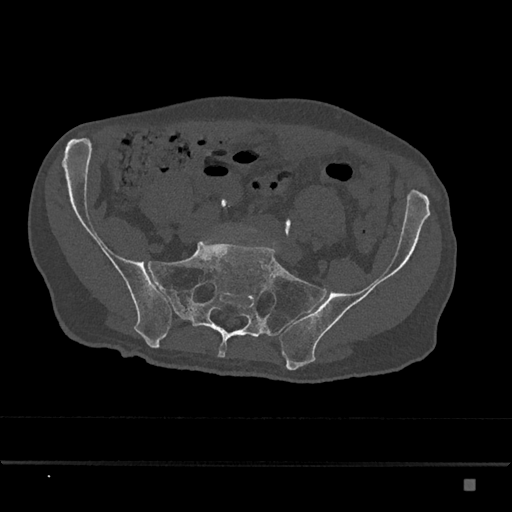
CT including the spine, one axial slice; slice 206 of 797 in the series (ordered by position); 120 kVp; bone window (W 1800 / L 400 HU); 0.5 mm slice thickness; 512 × 512 image matrix, field of view 390 × 390 mm. Male patient, age 72 years. From the clinical record (not read from this slice): primary cancer: prostate.
Outlined on this slice (semi-automatically segmented with operator editing):
- L5 vertebra: bounding box (x1, y1, x2, y2) in pixels: (236, 229, 252, 234)